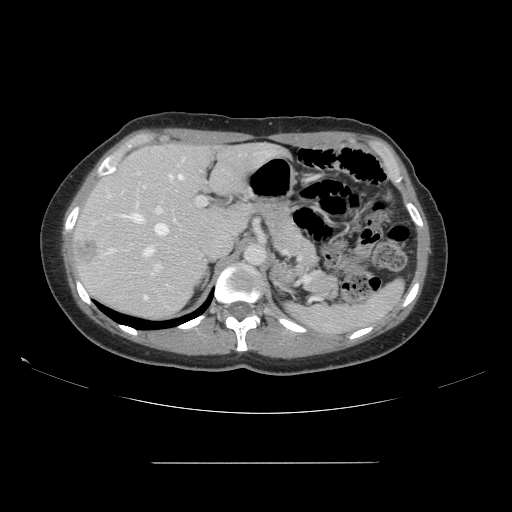
Contrast-enhanced abdominal CT, one axial slice; slice 104 of 151 in the series (ordered by position); 120 kVp; intravenous contrast given; soft-tissue window (W 400 / L 40 HU); 2.5 mm slice thickness; 512 × 512 image matrix, field of view 421 × 421 mm. Female patient, age 46 years. From the clinical record (not read from this slice): diagnosis: colorectal cancer liver metastases, imaged before liver resection; multiple liver metastases: yes; largest metastasis: 3 cm; disease in both lobes: yes.
Annotated regions visible in this slice (manually delineated by an expert):
- hepatic veins: bounding box (x1, y1, x2, y2) in pixels: (107, 174, 184, 257)
- liver: (72, 143, 279, 320)
- planned liver remnant (the part of the liver to remain after resection): (89, 144, 280, 255)
- portal vein (with intrahepatic branches): (138, 172, 207, 300)
- liver metastasis: (76, 241, 99, 265)